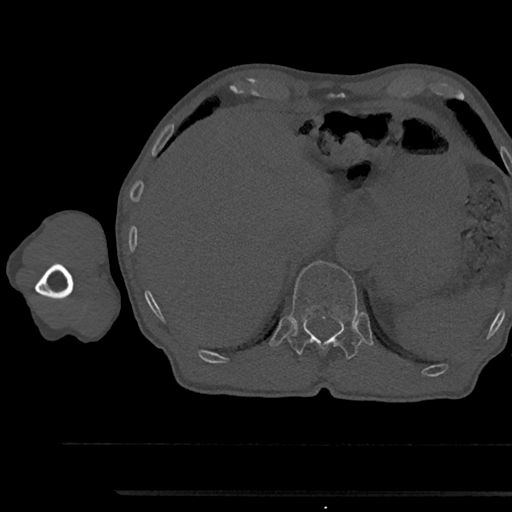
CT including the spine, one axial slice; position 723 of 797 along the scan axis; reconstruction kernel Br40s/3; 120 kVp; bone window (W 1800 / L 400 HU); 0.5 mm slice thickness; 512 × 512 image matrix, field of view 367 × 367 mm. Patient: male, 79 years. Case-level facts recorded for this patient, not image findings: primary cancer: prostate.
Outlined on this slice (semi-automatically segmented with operator editing):
- T12 vertebra: box from (x=288, y=261) to (x=362, y=358) px